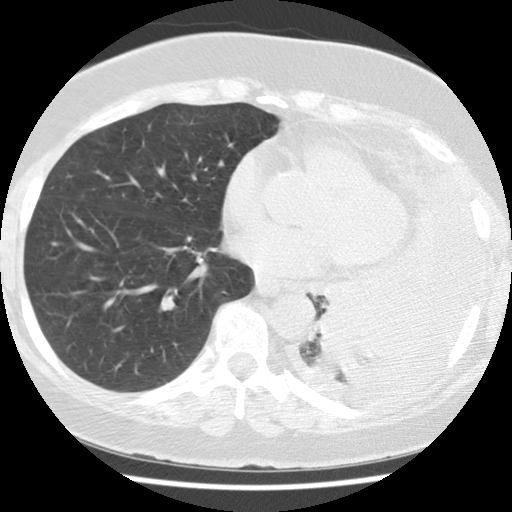
Chest CT (low-dose screening protocol), one axial image. Baseline annual screen. Lung window (W 1500 / L -600 HU). 2.5 mm slice thickness. Standard (soft-tissue) reconstruction kernel (STANDARD). 512 × 512 image matrix. Female, age 65 years at enrolment. Current smoker at enrolment.
- Lesion marked by an expert reader, bounding box [x1, y1, x2, y2] px = [313, 281, 434, 383].
- The exam's reader record, not a measurement of the box and not confirmed to be the same lesion: non-calcified nodule or mass ≥4 mm, left lower lobe, 74 × 48 mm, spiculated (stellate) margins, soft tissue attenuation.
- Official screen result: positive, change unspecified: nodule(s) >= 4 mm or enlarging nodule(s), mass(es), or other non-specific abnormalities suspicious for lung cancer.
- Lung cancer was diagnosed 13 days after this screen: adenocarcinoma, NOS, left lower lobe, stage IV (AJCC 6th edition), 74 mm at pathology.